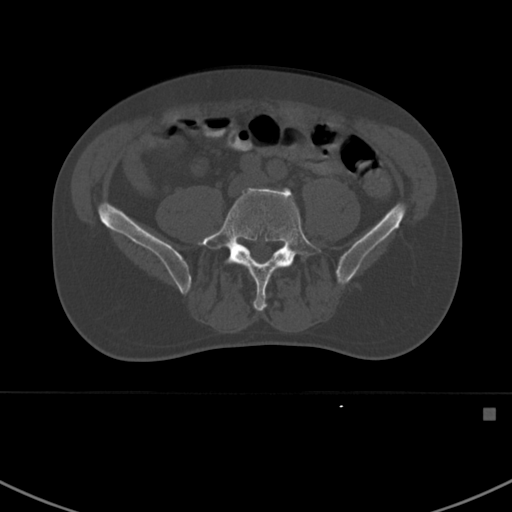
CT including the spine, one axial slice. Slice 221 of 412 in the series (ordered by position). 120 kVp. Bone window (W 1800 / L 400 HU). 1.5 mm slice thickness. 512 × 512 image matrix, field of view 358 × 358 mm. Male patient, age 59 years. From the clinical record (not read from this slice): primary cancer: prostate.
Outlined on this slice (semi-automatic segmentation, software-assisted and operator-edited):
- L5 vertebra: box from (x=200, y=187) to (x=321, y=312) px